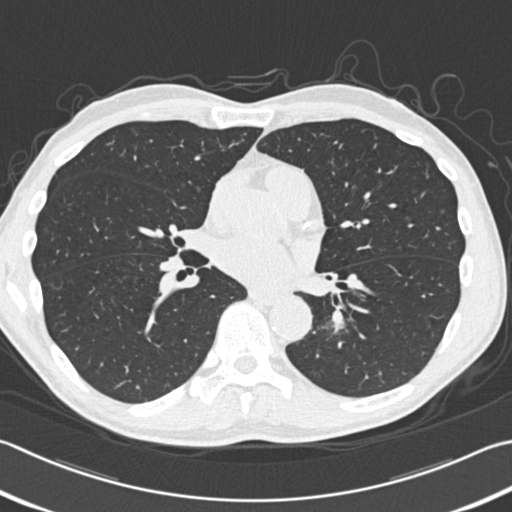
Low-dose screening chest CT, one axial slice. Position 171 of 354 along the scan axis. 120 kVp. Lung window (W 1500 / L -600 HU). 512 × 512 image matrix, field of view 346 × 346 mm.
Outlined on this slice (manually delineated by an expert):
- lesion 1 (tumor, lower lobe of left lung): bounding box [x1, y1, x2, y2] px = [333, 312, 344, 331]